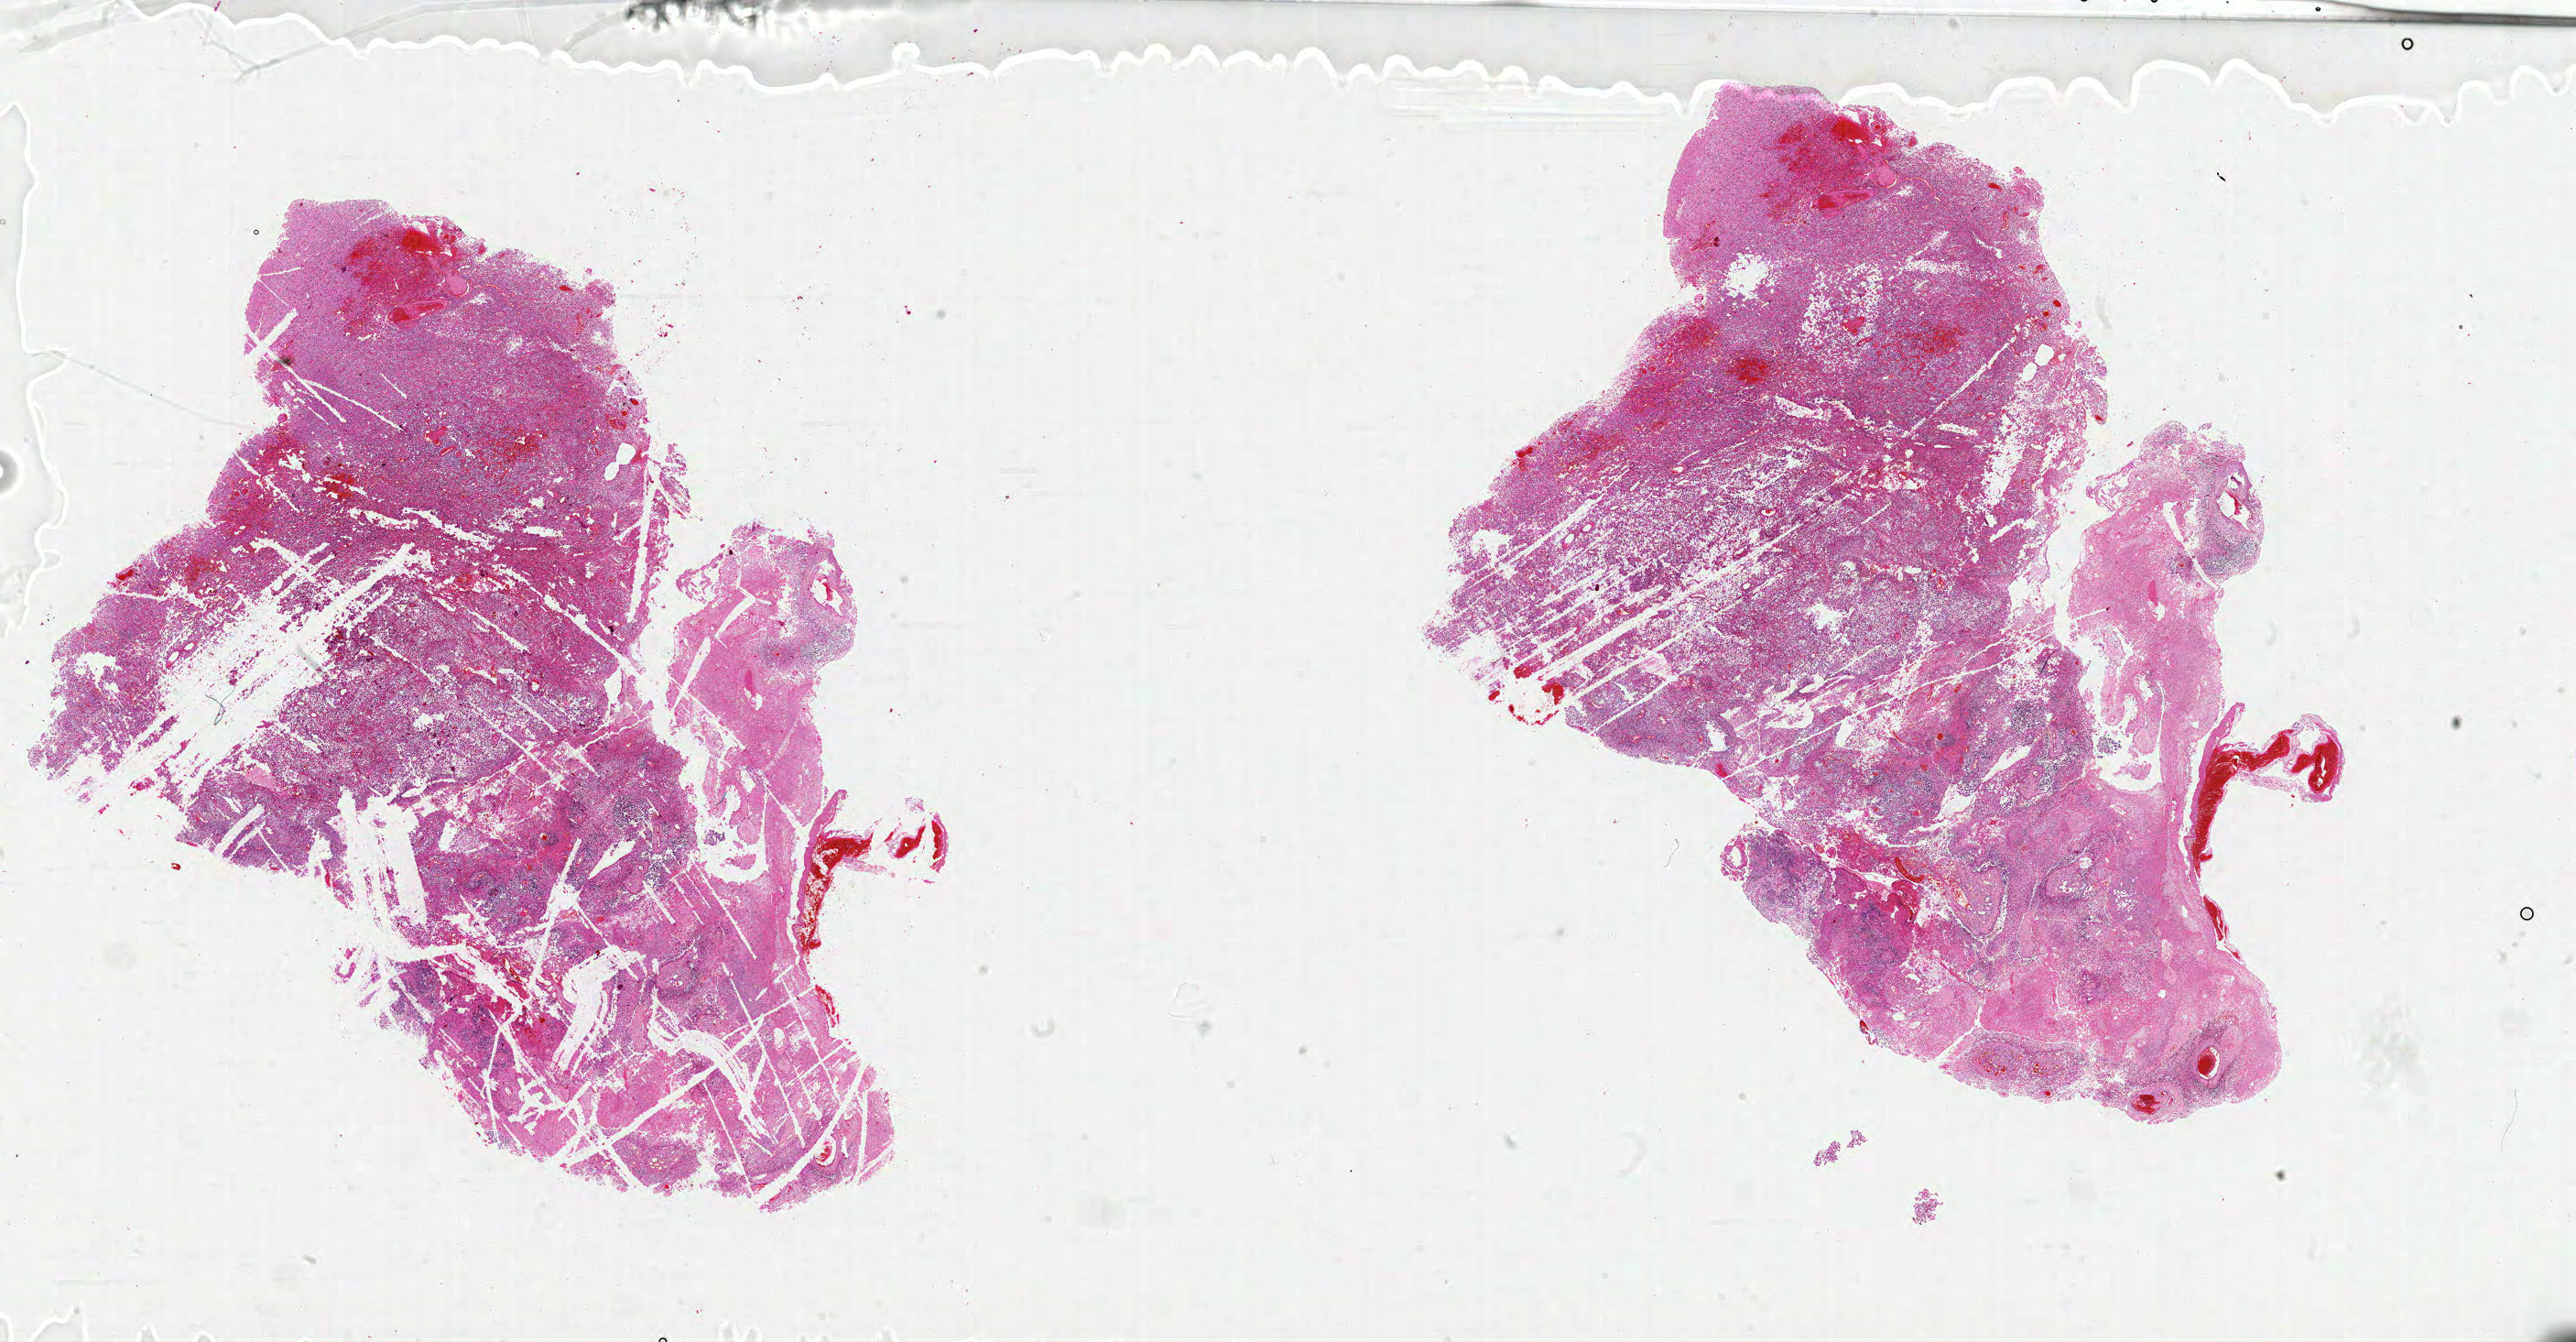
H&E-stained whole-slide image, a low-resolution overview of the entire scanned area, about 45.0 x 23.4 mm; formalin-fixed paraffin-embedded (FFPE) diagnostic section; sample: primary tumour, brain. Male, age 58 years at initial diagnosis.
* pathologic diagnosis: Glioblastoma